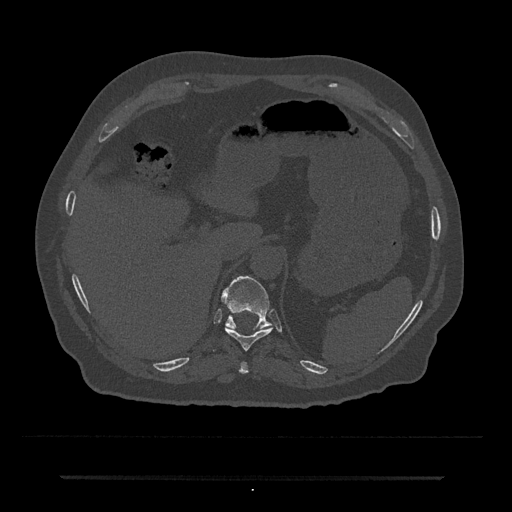
CT including the spine, one axial slice; position 213 of 797 along the scan axis; 120 kVp; bone window (W 1800 / L 400 HU); 0.5 mm slice thickness; 512 × 512 image matrix. Patient: male, 69 years. Case-level facts recorded for this patient, not image findings: primary cancer: prostate.
Outlined on this slice (semi-automatically segmented with operator editing):
- T10 vertebra: bounding box (x1, y1, x2, y2) in pixels: (214, 326, 273, 351)
- T11 vertebra: (221, 276, 272, 329)
- T9 vertebra: (239, 361, 249, 374)